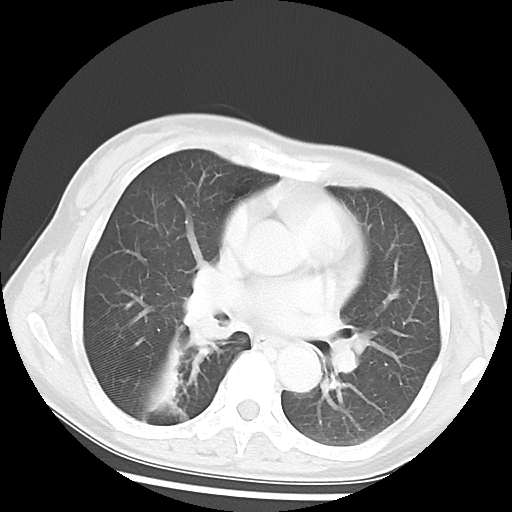
Chest CT, one axial slice; slice 29 of 52 in the series (ordered by position); reconstruction kernel LUNG; 120 kVp; lung window (W 1500 / L -600 HU); 5 mm slice thickness; 512 × 512 image matrix. Female patient, age 54 years. Case-level facts recorded for this patient, not image findings: clinical TNM (as recorded): T1c N0 M0; histopathological grade: G1-2.
Outlined on this slice (bounding box drawn by a radiologist):
- lung tumour (recorded histology: squamous cell carcinoma): bounding box <181,275,245,353> (left, top, right, bottom; pixels)